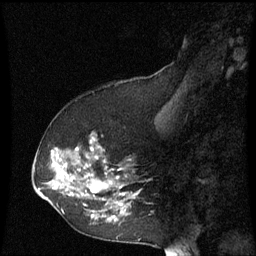
Breast MRI (dynamic contrast-enhanced), one sagittal slice; slice 24 of 60 in the series (ordered by position); dynamic contrast-enhanced series, image 2 of 3 at this slice position (ordered by acquisition); 1.5 T; TE 4.2 ms, TR 8.9 ms; 2 mm slice thickness; 256 × 256 image matrix, field of view 200 × 200 mm. Female patient, age 53 years. From the clinical record (not read from this slice): setting: breast cancer imaged before/during neoadjuvant chemotherapy; receptor status: HR-positive, HER2-negative.
Annotated regions visible in this slice (semi-automatically segmented with operator editing):
- analysis volume of interest (the breast-tissue region the enhancement analysis was run in; not a lesion): box from (x=38, y=134) to (x=151, y=227) px
- tumour enhancement mask (voxels above the 70 % enhancement threshold inside the analysis volume of interest): (x=52, y=138)–(x=139, y=221)